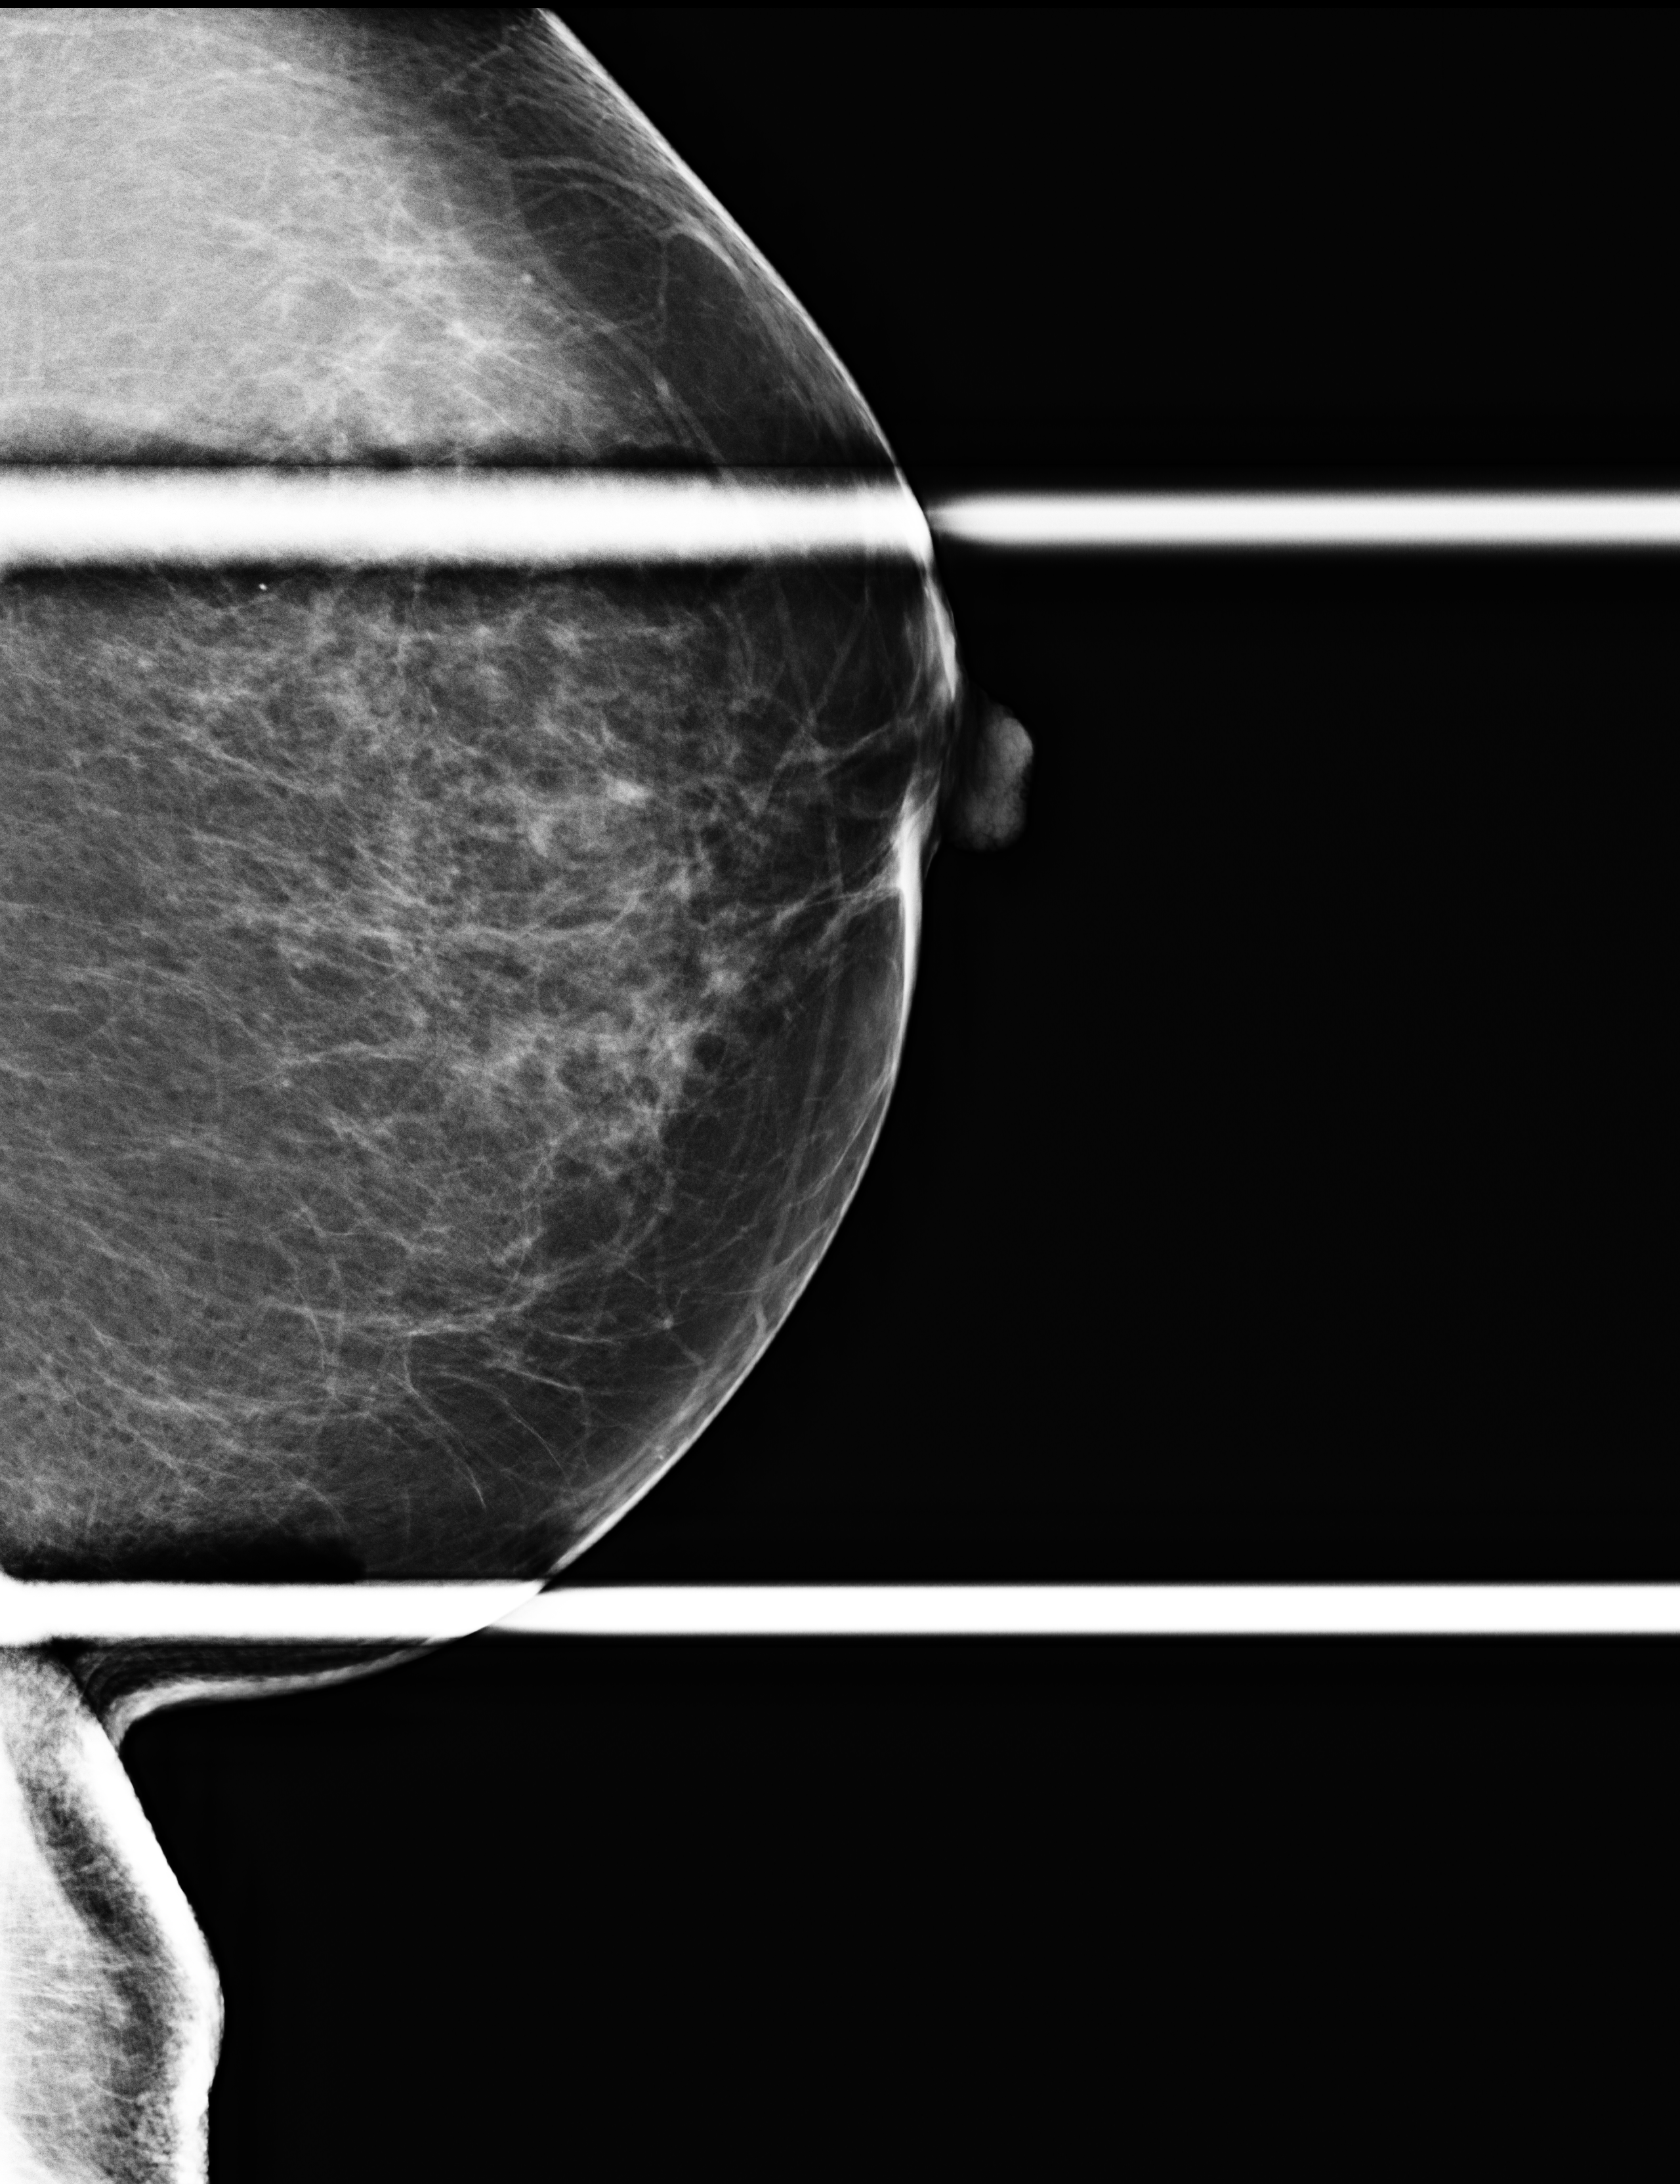
Additional work-up view, compressed breast thickness 68 mm. Female patient, age 74 years.
Image type: full-field digital mammogram. Breast: left. Projection: ML view, spot compression. BI-RADS breast density category at the screening exam (both breasts, scale 1–4): 3. Final BI-RADS category for the screening round (tomosynthesis exam, both breasts): category 4. Recall: recalled for additional imaging after this screen.